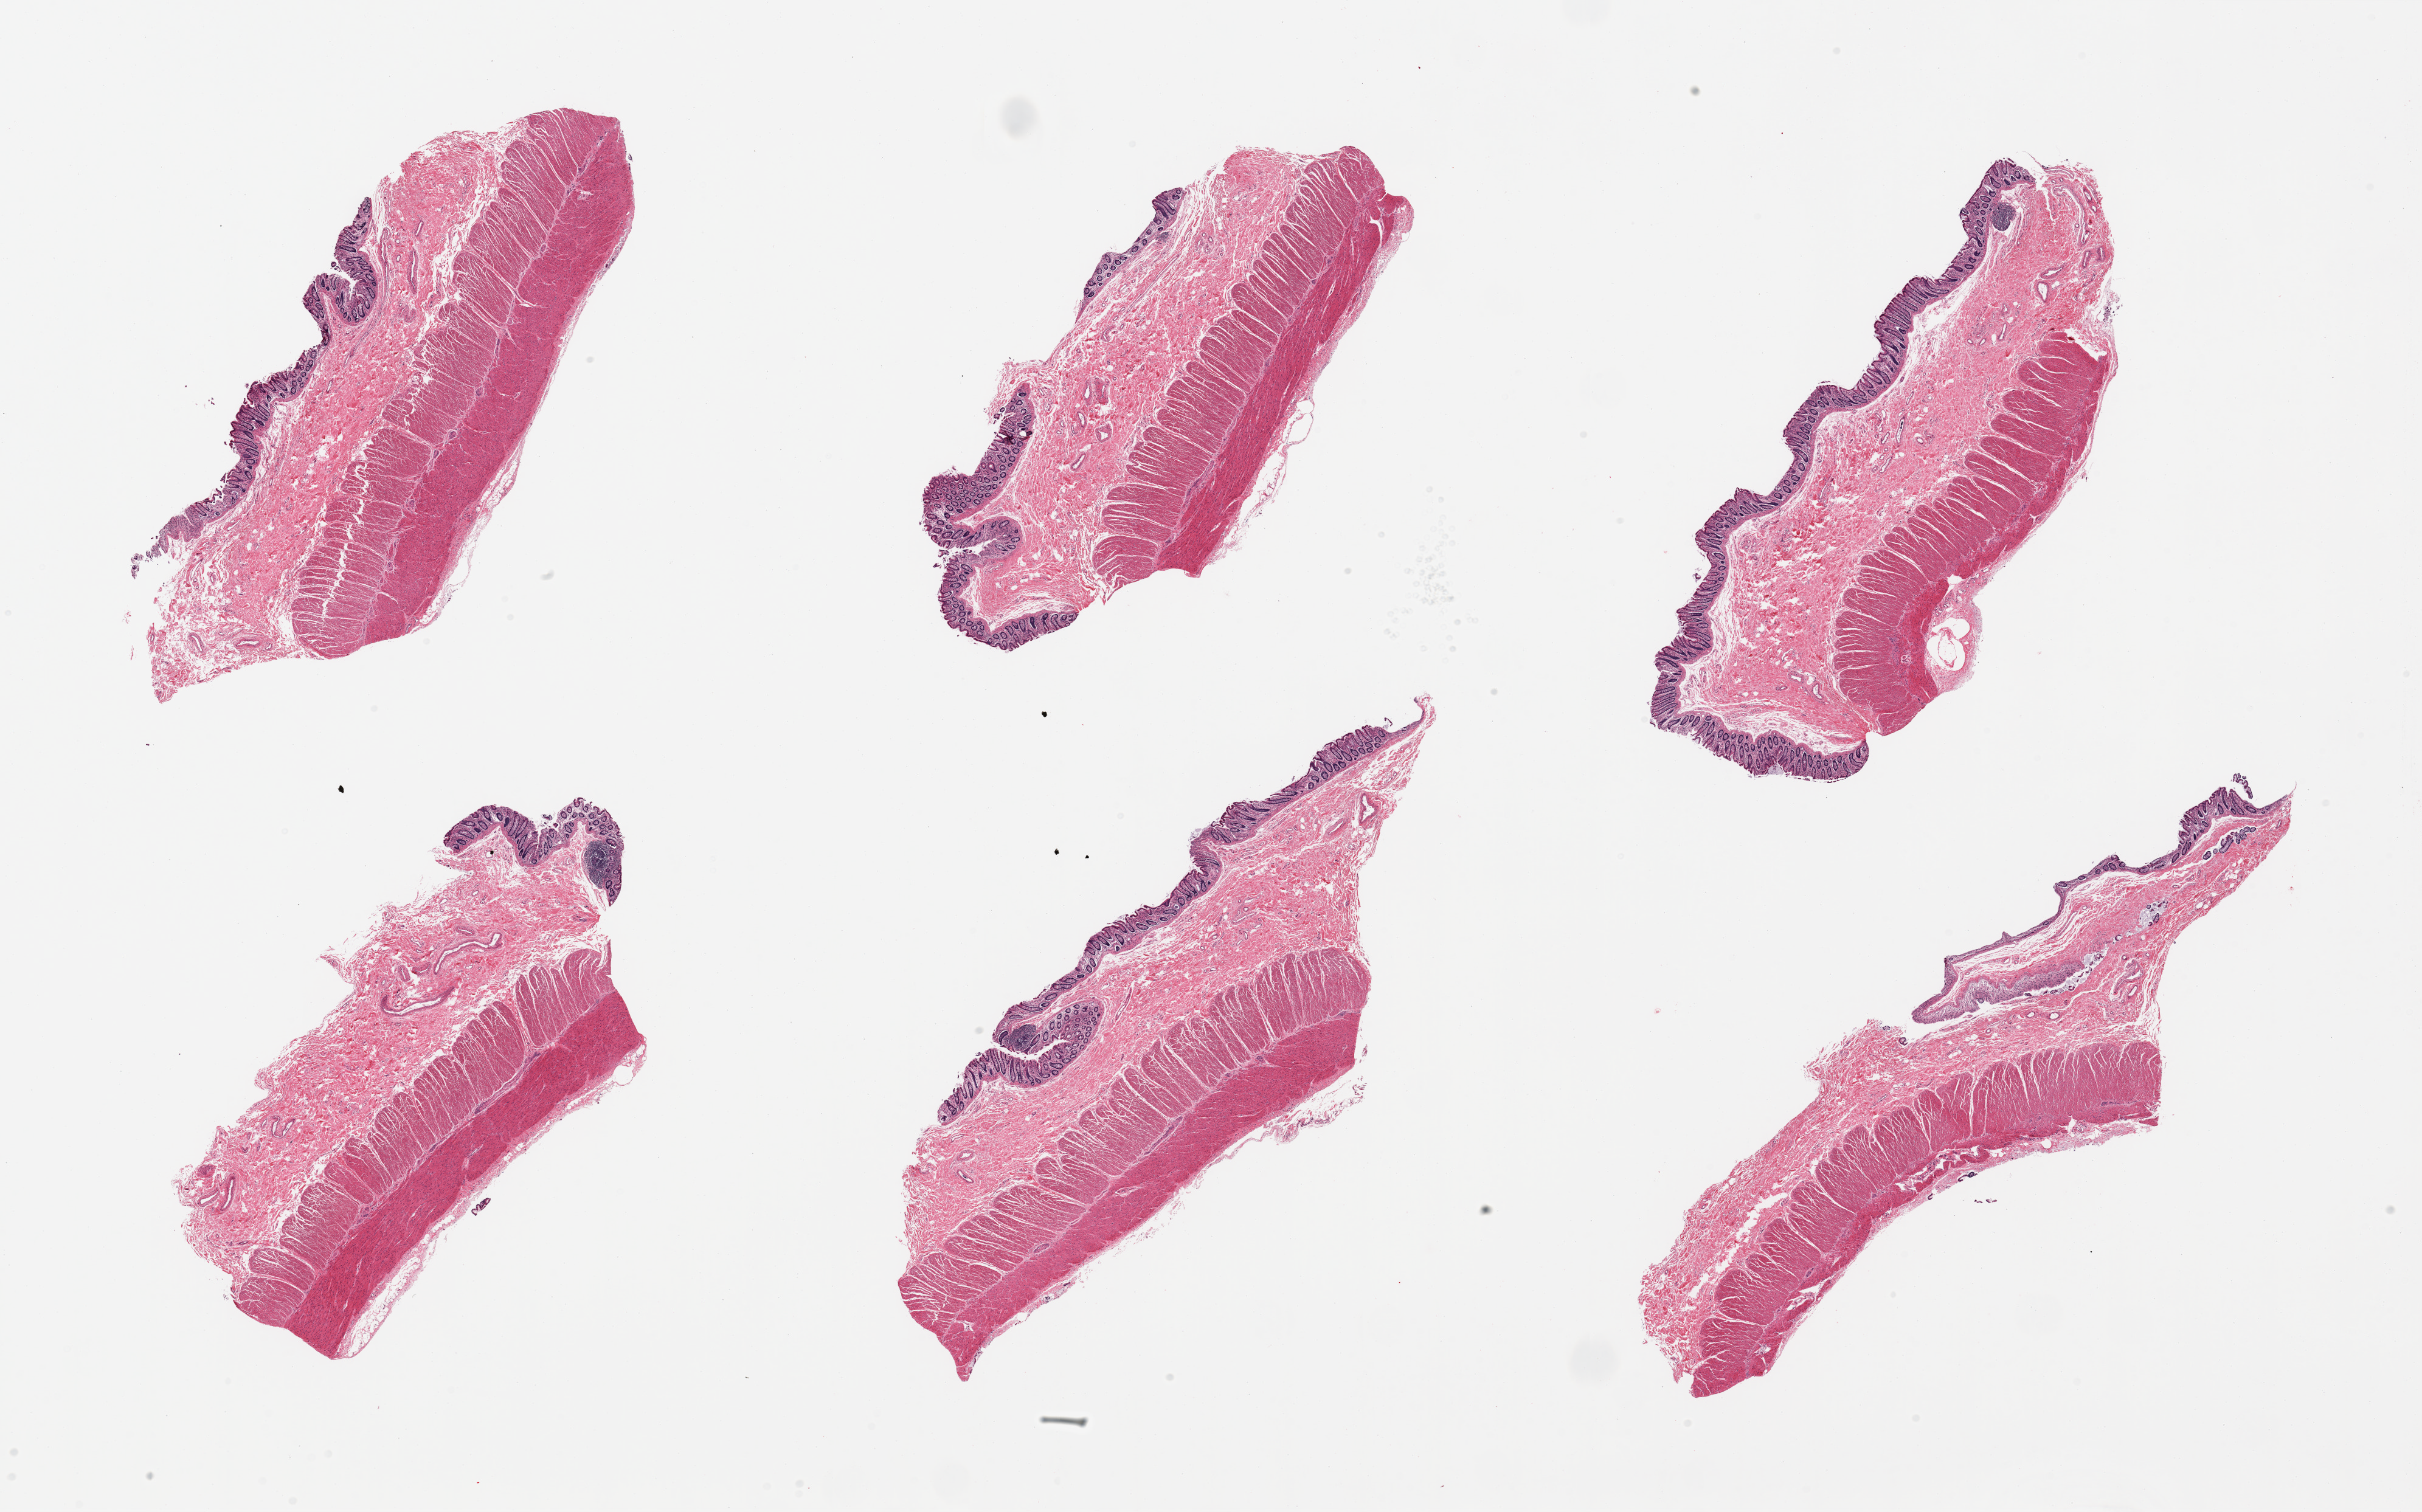
Hematoxylin and eosin (H&E) whole-slide image — low-resolution overview of the scanned area, about 31.5 x 19.7 mm, PAXgene-fixed paraffin-embedded (PFPE) section, target tissue: transverse colon, tissue donor sample. Donor sex: female.
• pathologist's review note for this sample: 6 pieces; mostly well preserved, mucosa and muscularis